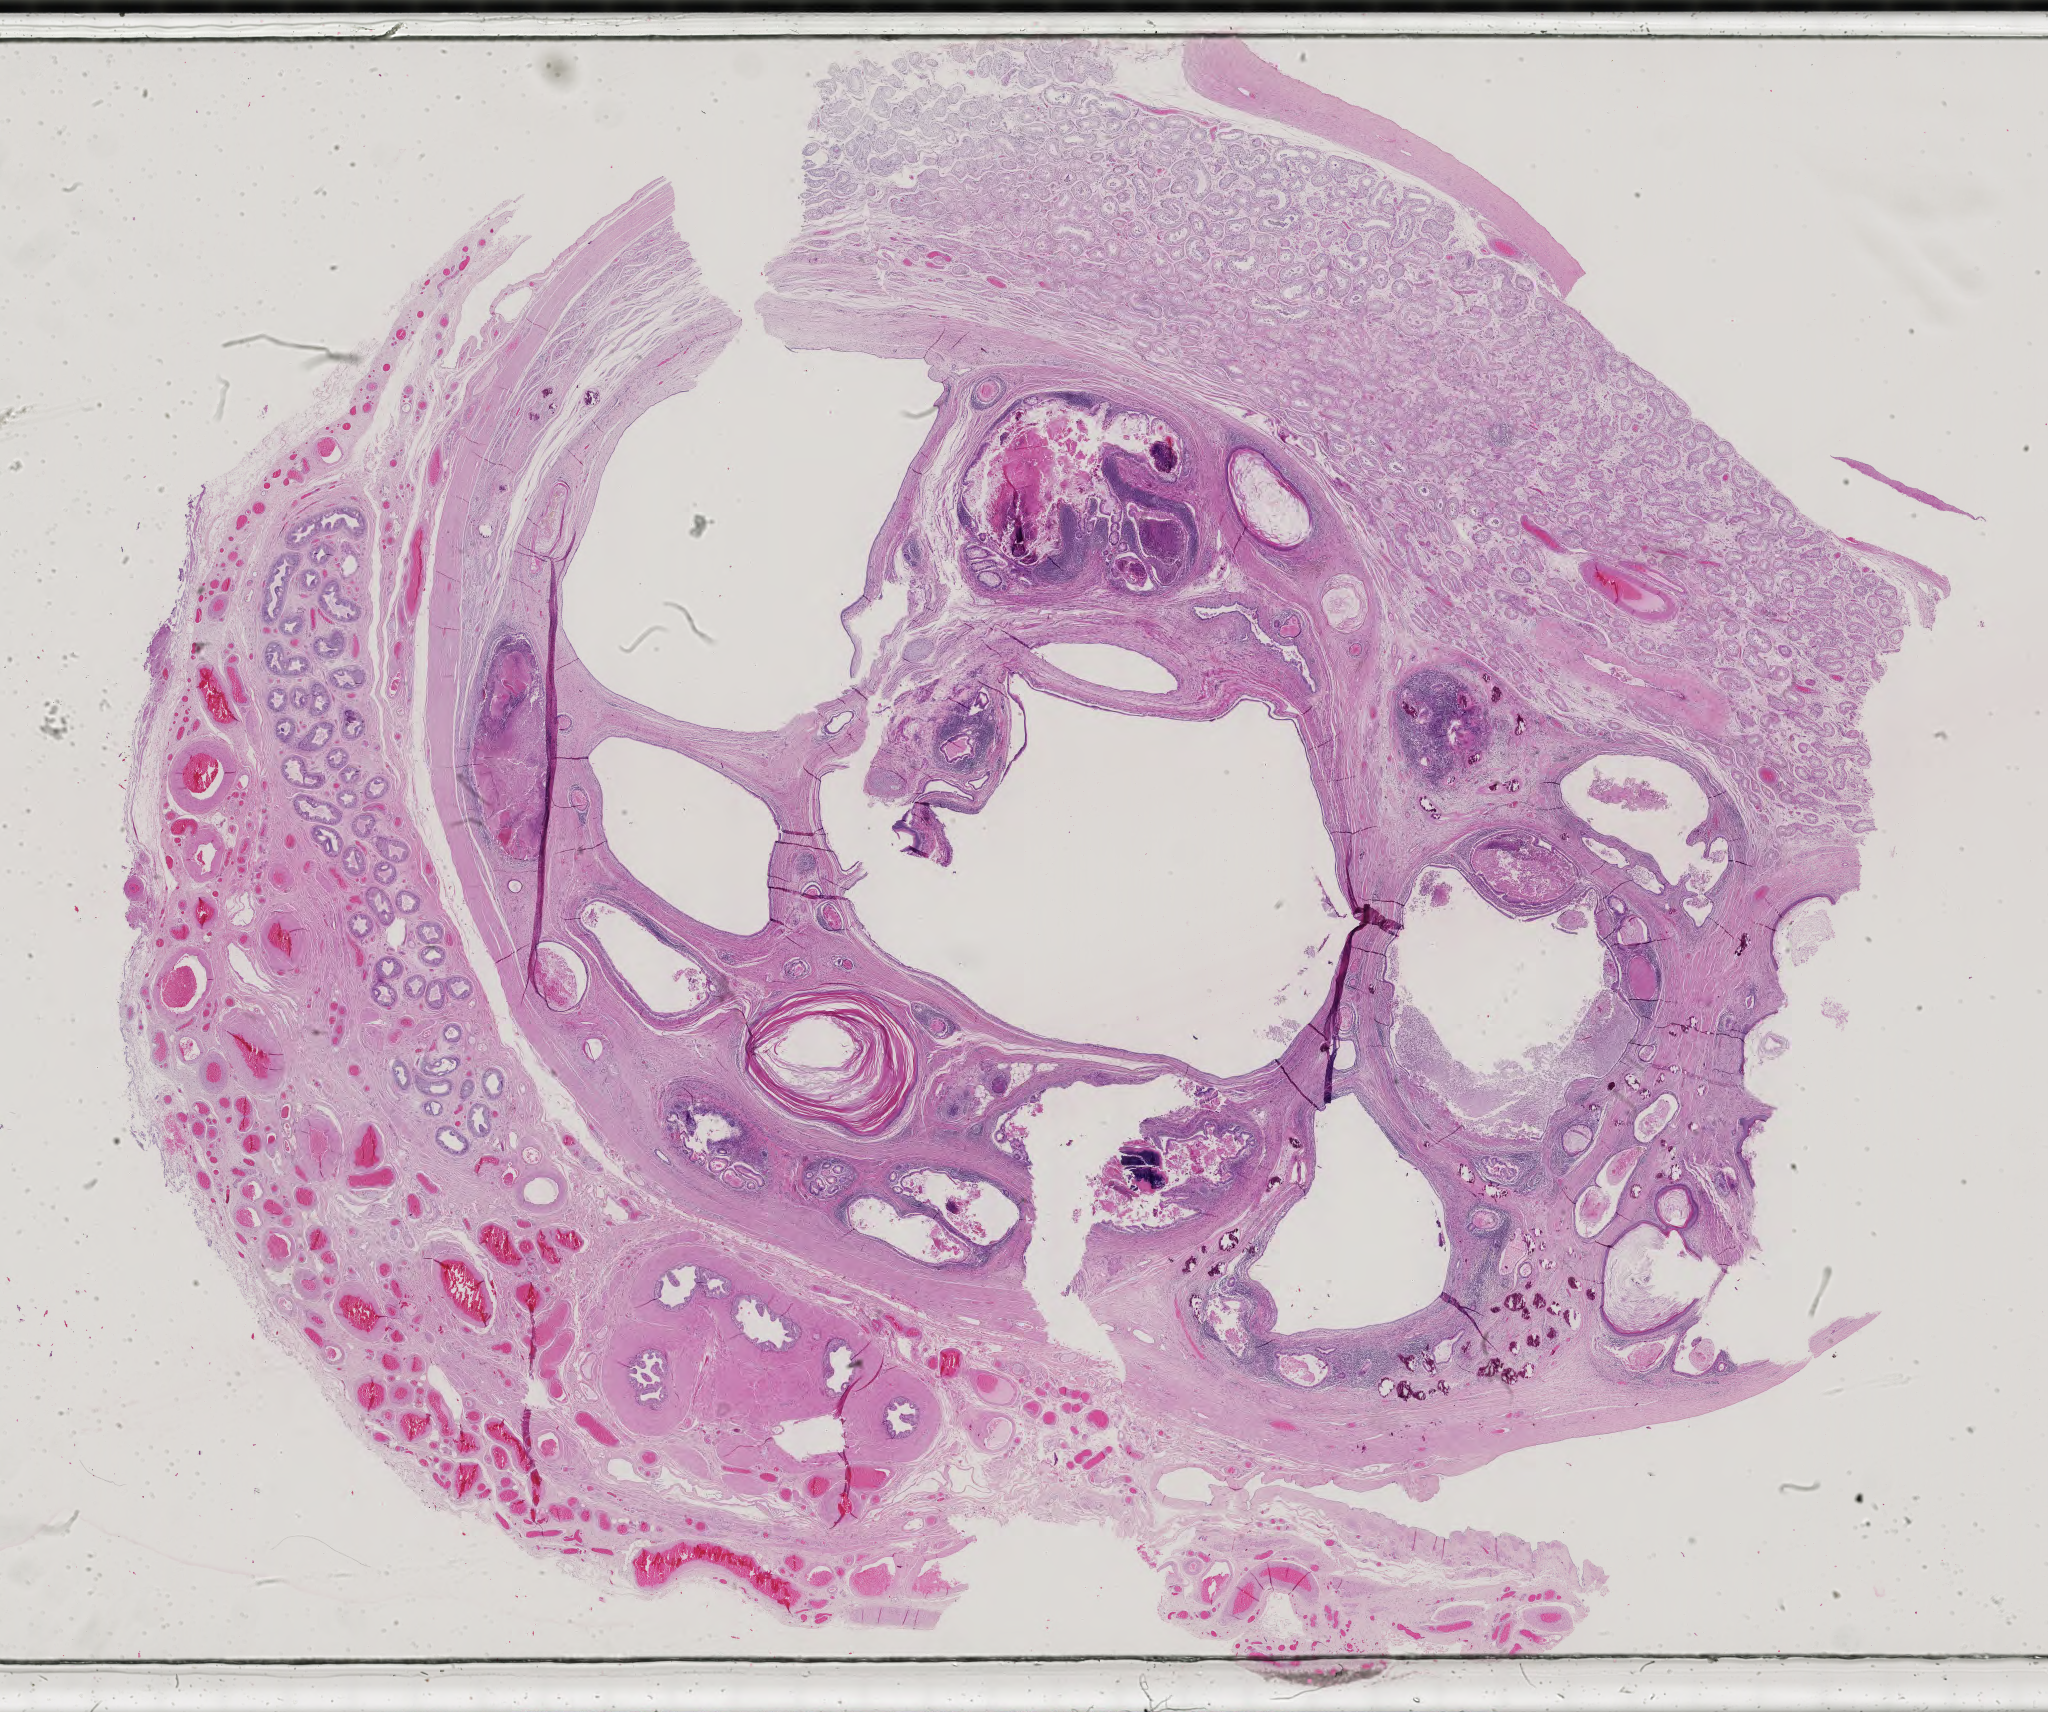
Whole-slide histology image, Hematoxylin and eosin (H&E) stained — a low-resolution overview of the entire scanned area, about 29.8 x 24.9 mm (from a 40x scan). Male patient.
Specimen: formalin-fixed paraffin-embedded (FFPE) diagnostic section; testis, primary tumour sample.